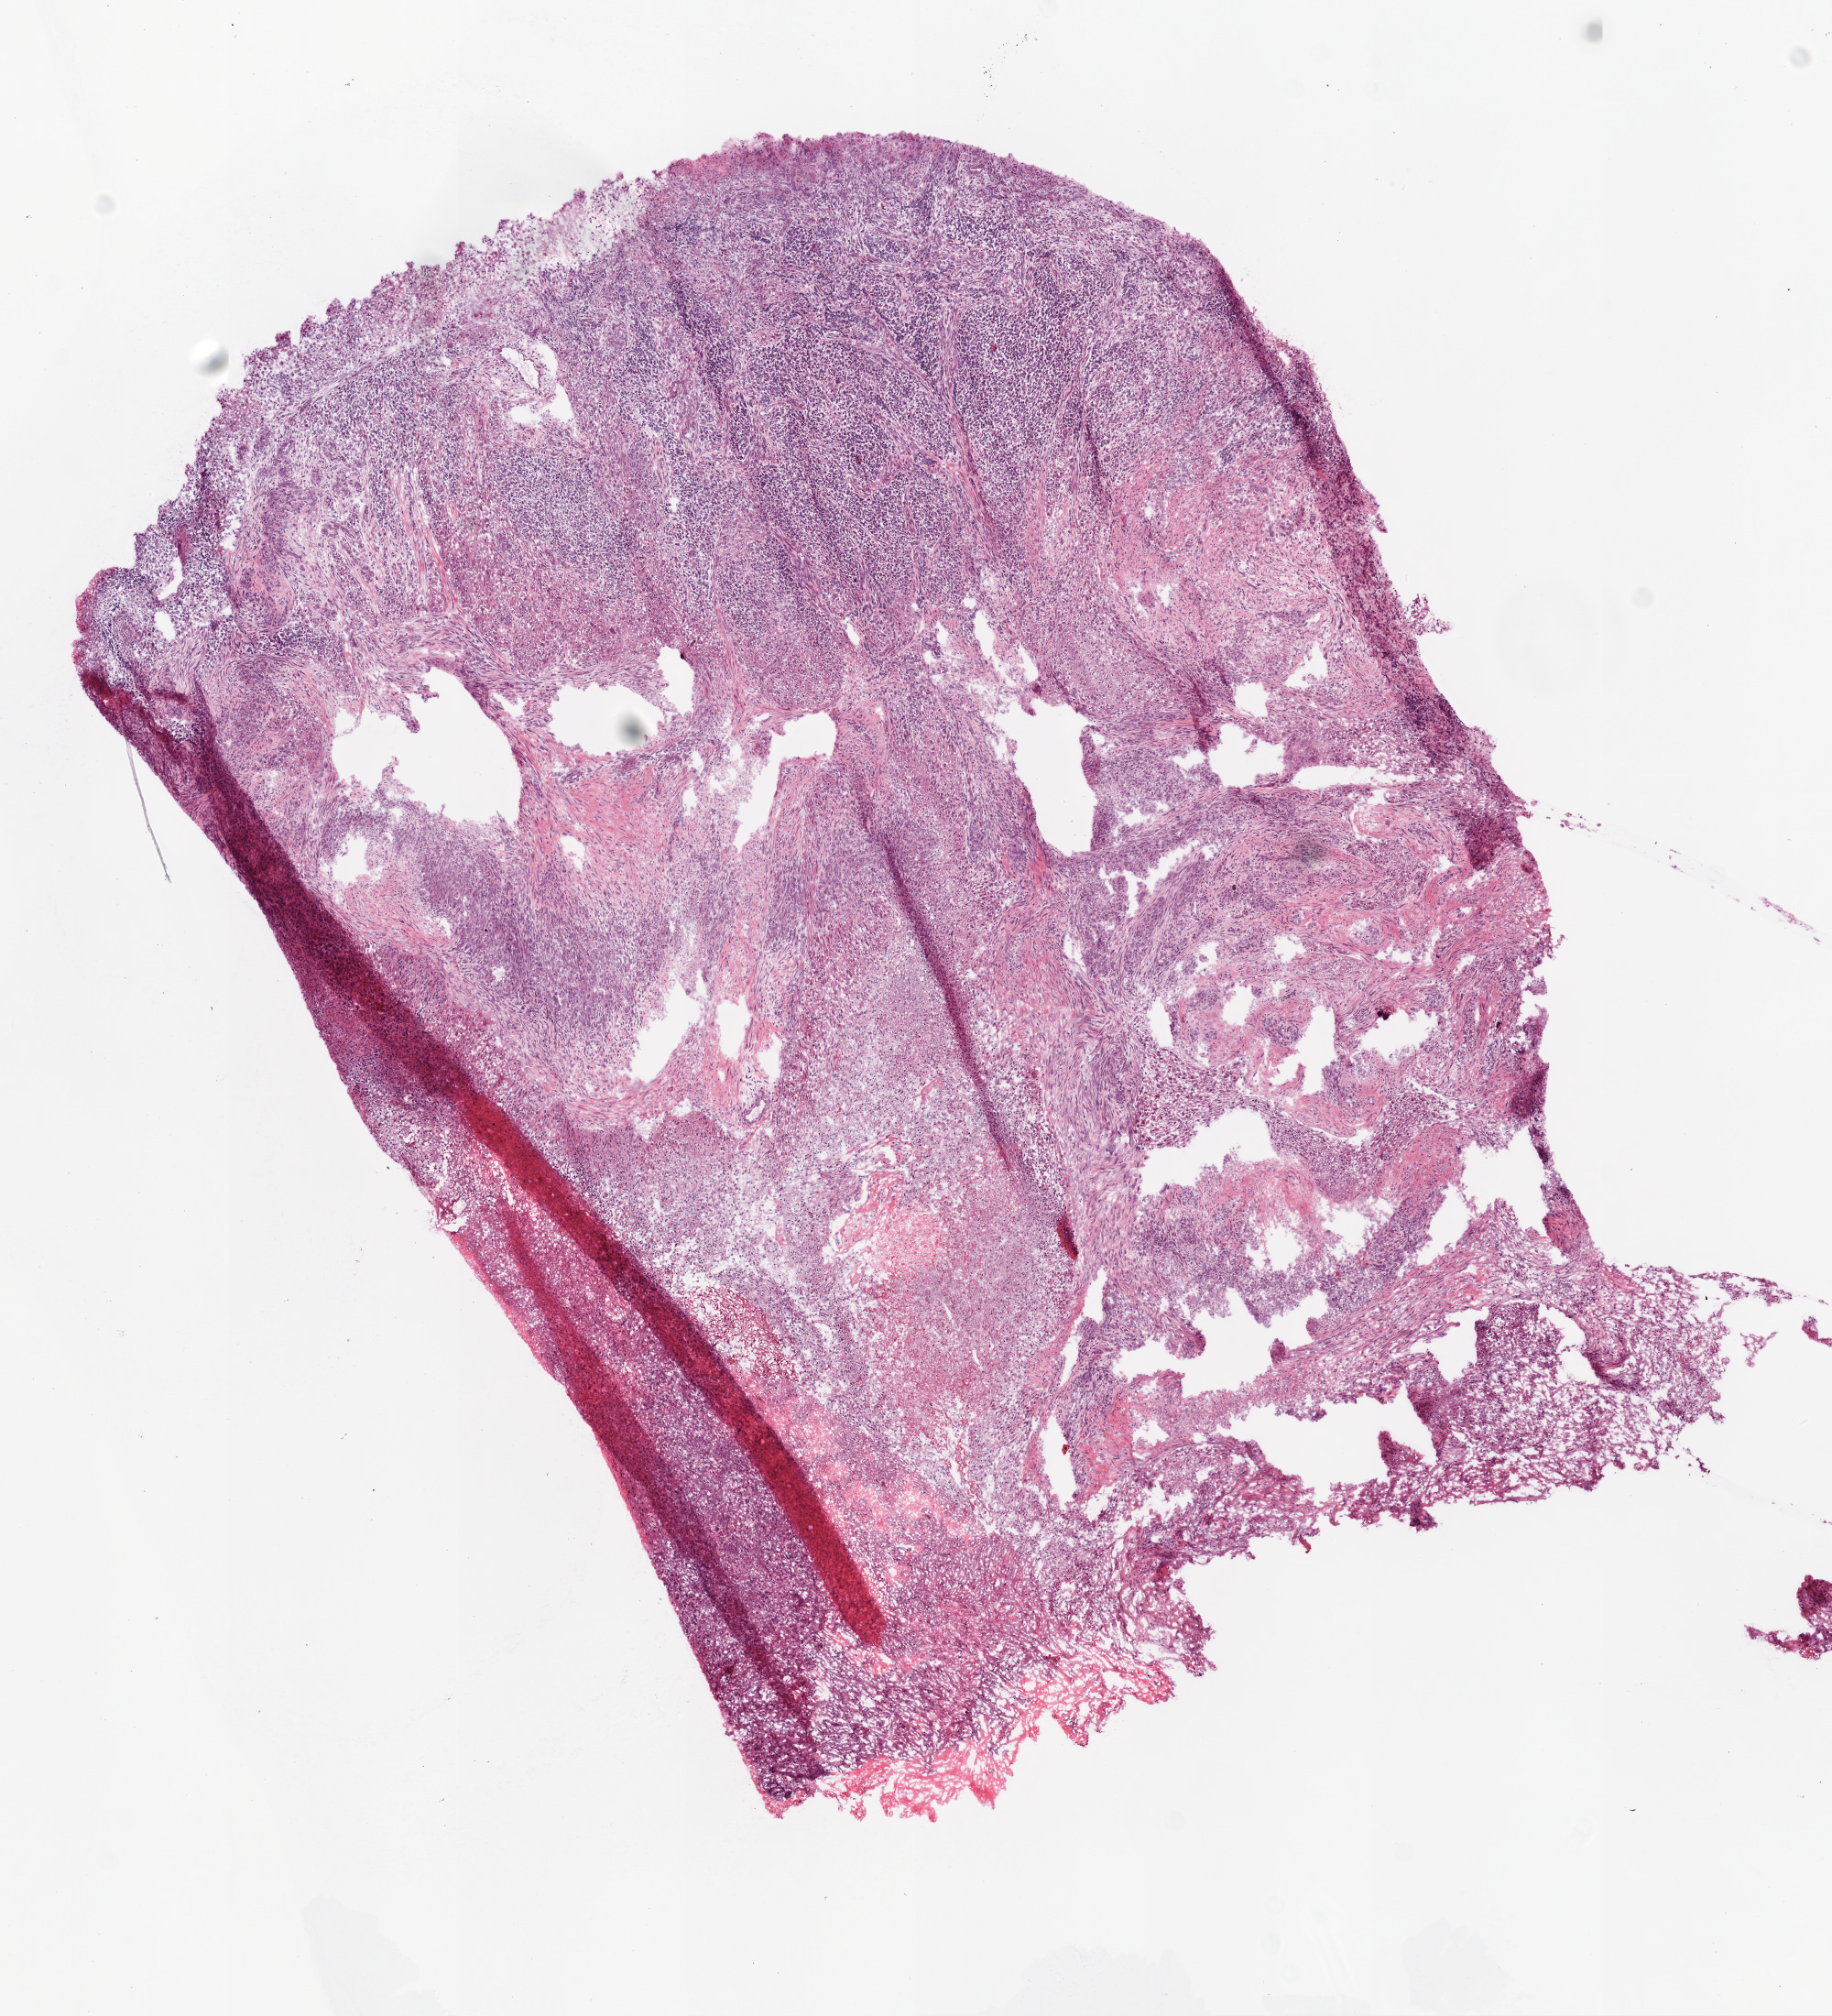
Whole-slide histology image, Hematoxylin and eosin (H&E) stained, low-resolution overview of the scanned area, about 8.0 x 8.8 mm, frozen section from the top of the tissue portion, sample: primary tumour, brain. Male patient; age at initial diagnosis 61 years. Slide review estimates, as recorded: tumour cells 65%, tumour nuclei 80%, normal cells 5%, stromal cells 20%, necrosis 10%.
• histologic diagnosis: Glioblastoma